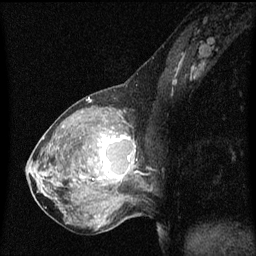
Breast MRI (dynamic contrast-enhanced), one sagittal slice. Dynamic contrast-enhanced series, image 2 of 3 at this slice position (ordered by acquisition). 1.5 T. TE 4.2 ms, TR 8 ms. 256 × 256 image matrix, field of view 200 × 200 mm. Patient: female, 50 years.
Outlined on this slice (semi-automatic segmentation, software-assisted and operator-edited):
- analysis volume of interest (the breast-tissue region the enhancement analysis was run in; not a lesion): bounding box [x1, y1, x2, y2] px = [91, 126, 141, 189]
- tumour enhancement mask (voxels above the 70 % enhancement threshold inside the analysis volume of interest): [92, 134, 135, 181]